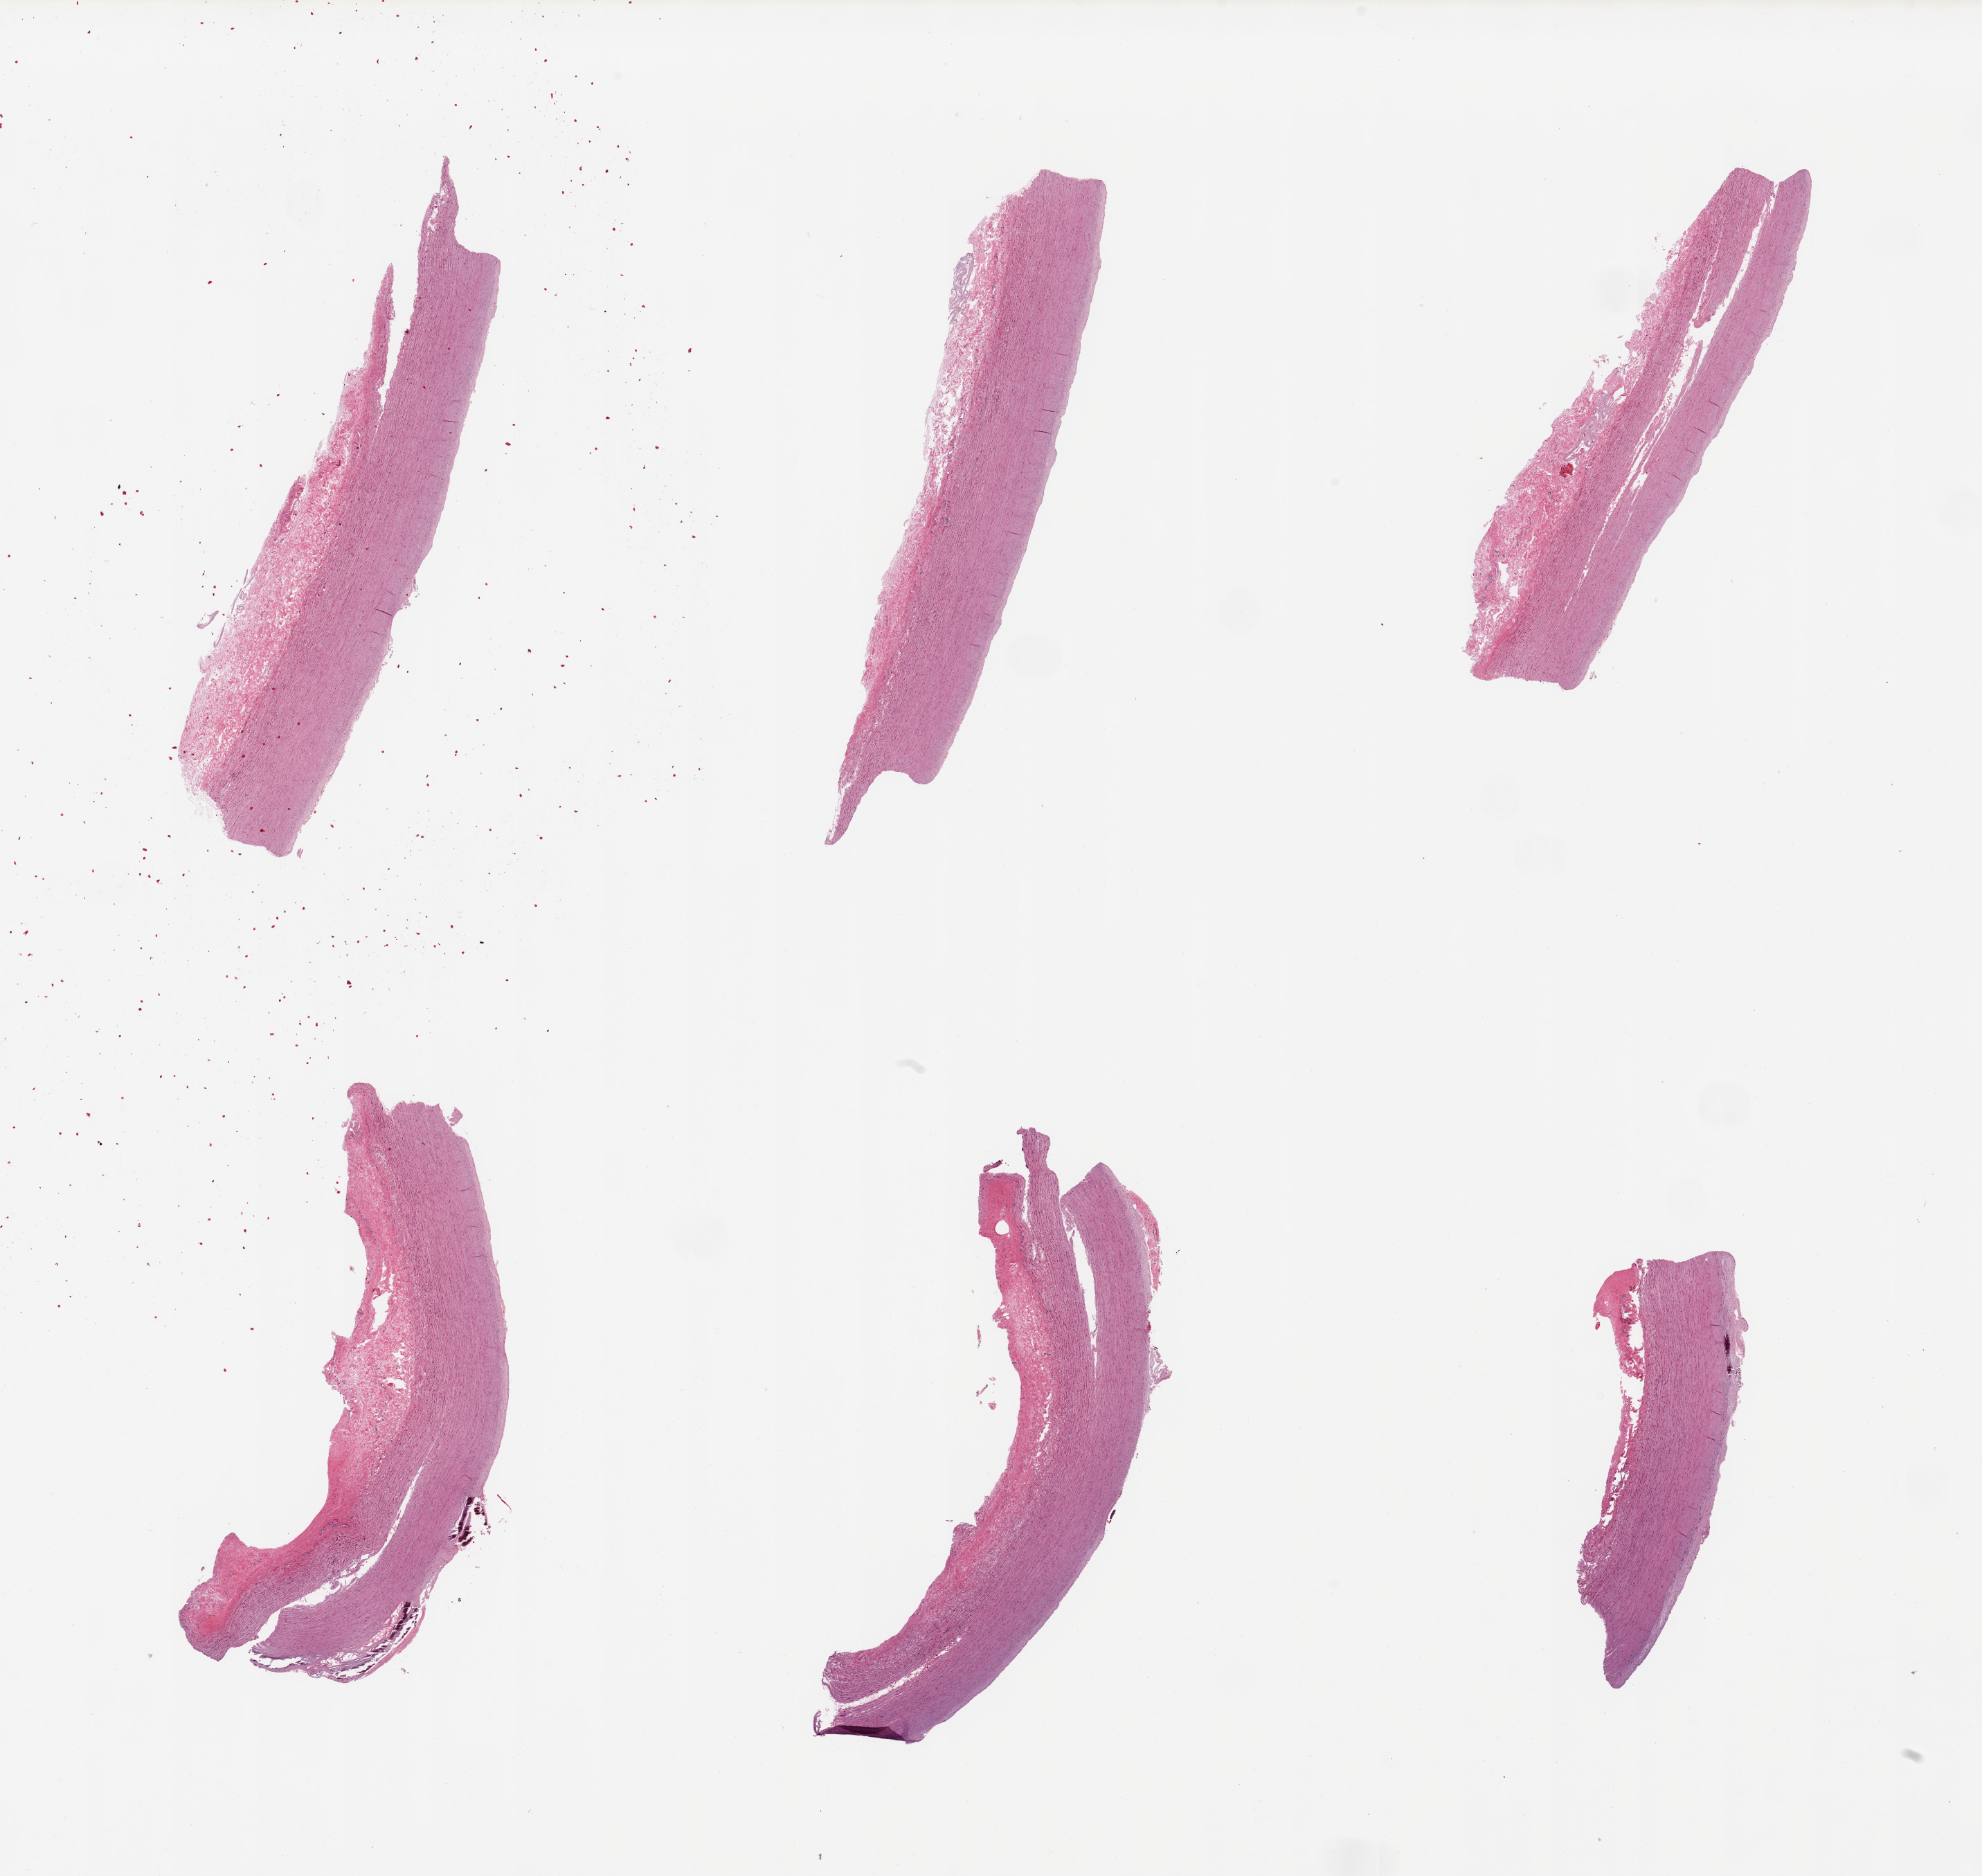
Digitized hematoxylin and eosin (H&E)-stained section, brightfield, low-resolution overview of the scanned area, about 22.6 x 21.4 mm, PAXgene-fixed, paraffin-embedded tissue, target tissue: aorta, donor tissue sample.
Pathologist's review note for this sample: 2 pieces, focal calcifying atheromatous deposits.